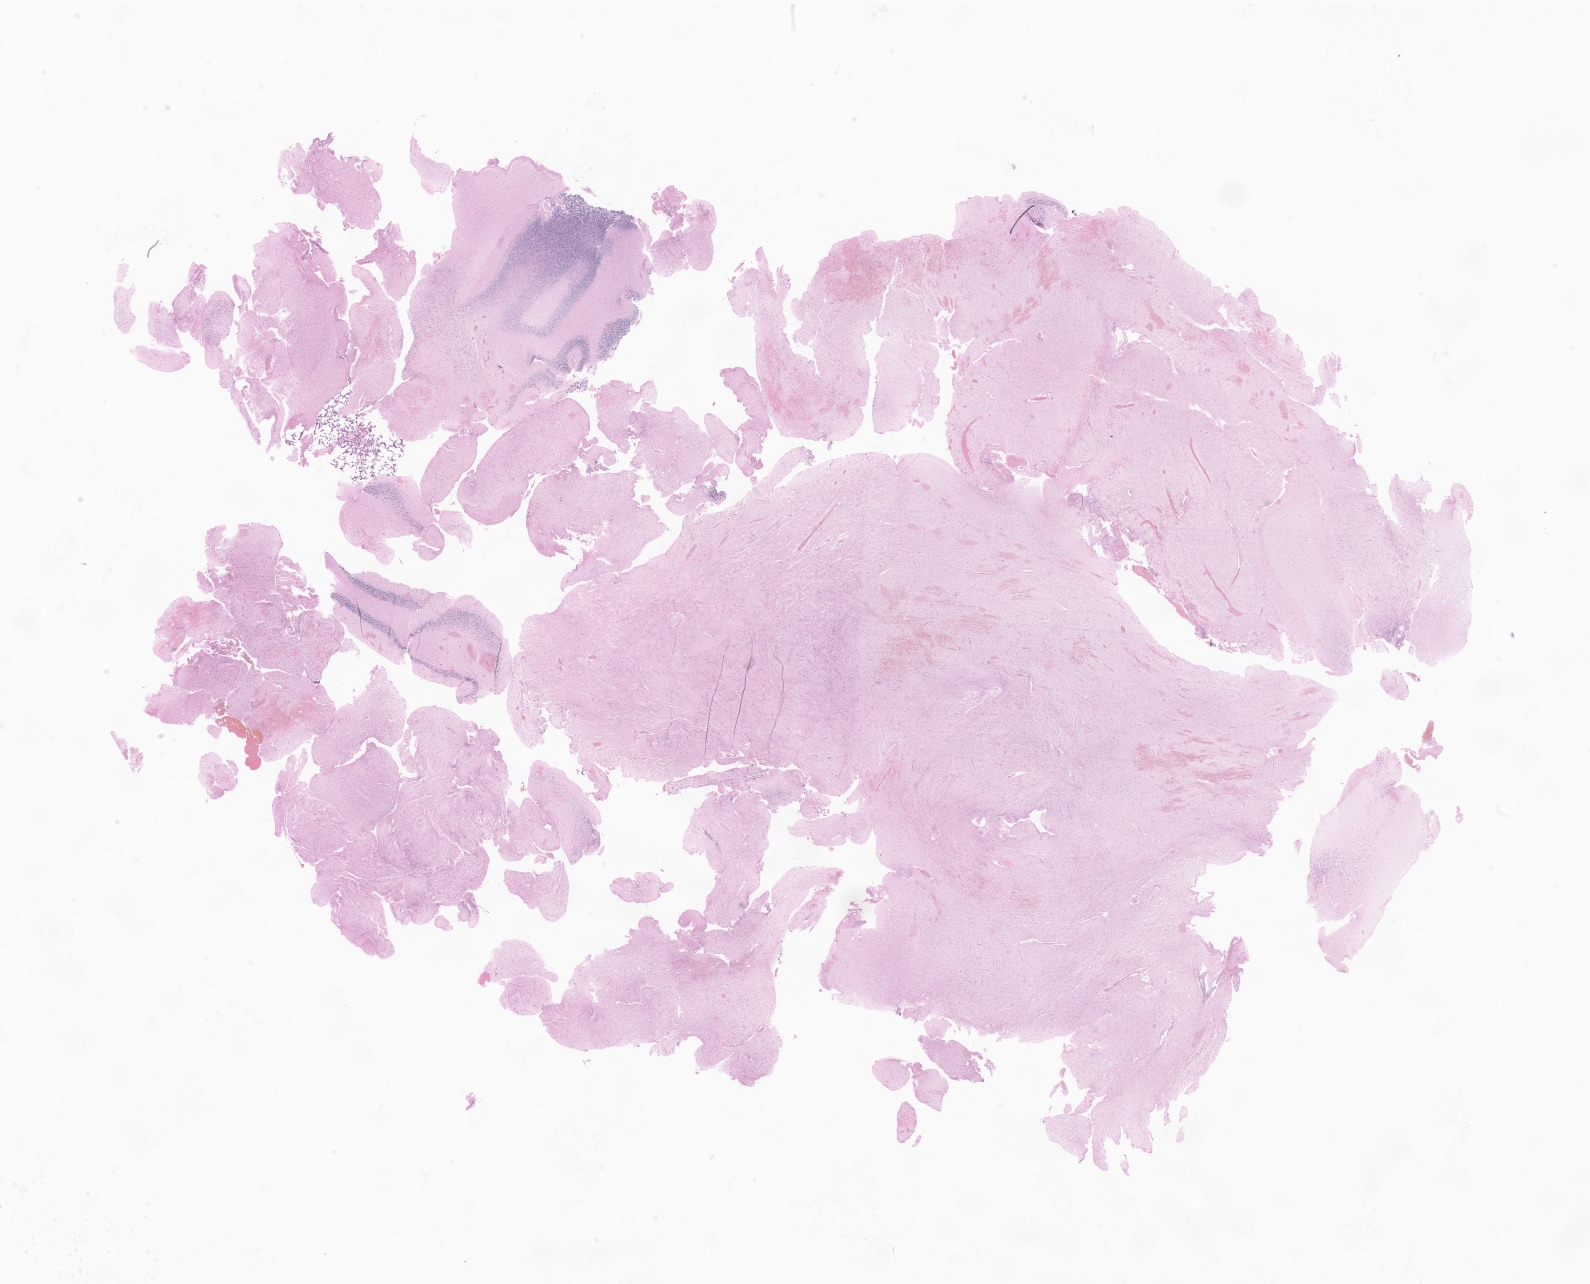
H&E whole-slide image of tumor tissue from the cerebellum, whole scanned area (about 26.8 x 21.7 mm) shown as a low-resolution overview, FFPE section. Patient: female, age 175 months.
Diagnosis (ICD-O-3 morphology term): Pilocytic astrocytoma.